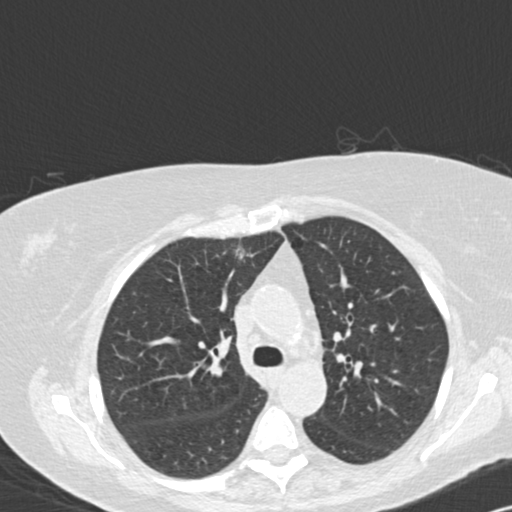
Axial slice from a low-dose chest CT screening exam, third screening round (two years after baseline), lung window (W 1500 / L -600 HU), 2 mm slice thickness, 120 kVp, slice 43 of 141 in the series. Female participant, aged 72 years at enrolment.
Expert reader's lesion annotation, box from (x=219, y=235) to (x=266, y=278) px. Reader record for this screening exam (exam-level; its link to the box is not recorded): non-calcified nodule or mass ≥4 mm, right upper lobe, 8 × 8 mm, spiculated (stellate) margins, soft tissue attenuation, pre-existing on the prior screen: yes; interval growth: yes.